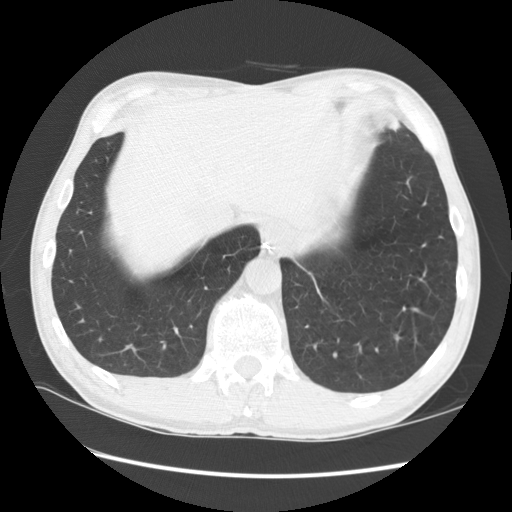
Low-dose screening chest CT, one axial slice; position 25 of 141 along the scan axis; reconstruction kernel STANDARD; lung window (W 1500 / L -600 HU); 2.5 mm slice thickness; 512 × 512 image matrix.
Annotated regions visible in this slice (manually delineated by an expert):
- lesion 1 (tumor, lower lobe of left lung): box from (x=388, y=121) to (x=401, y=132) px